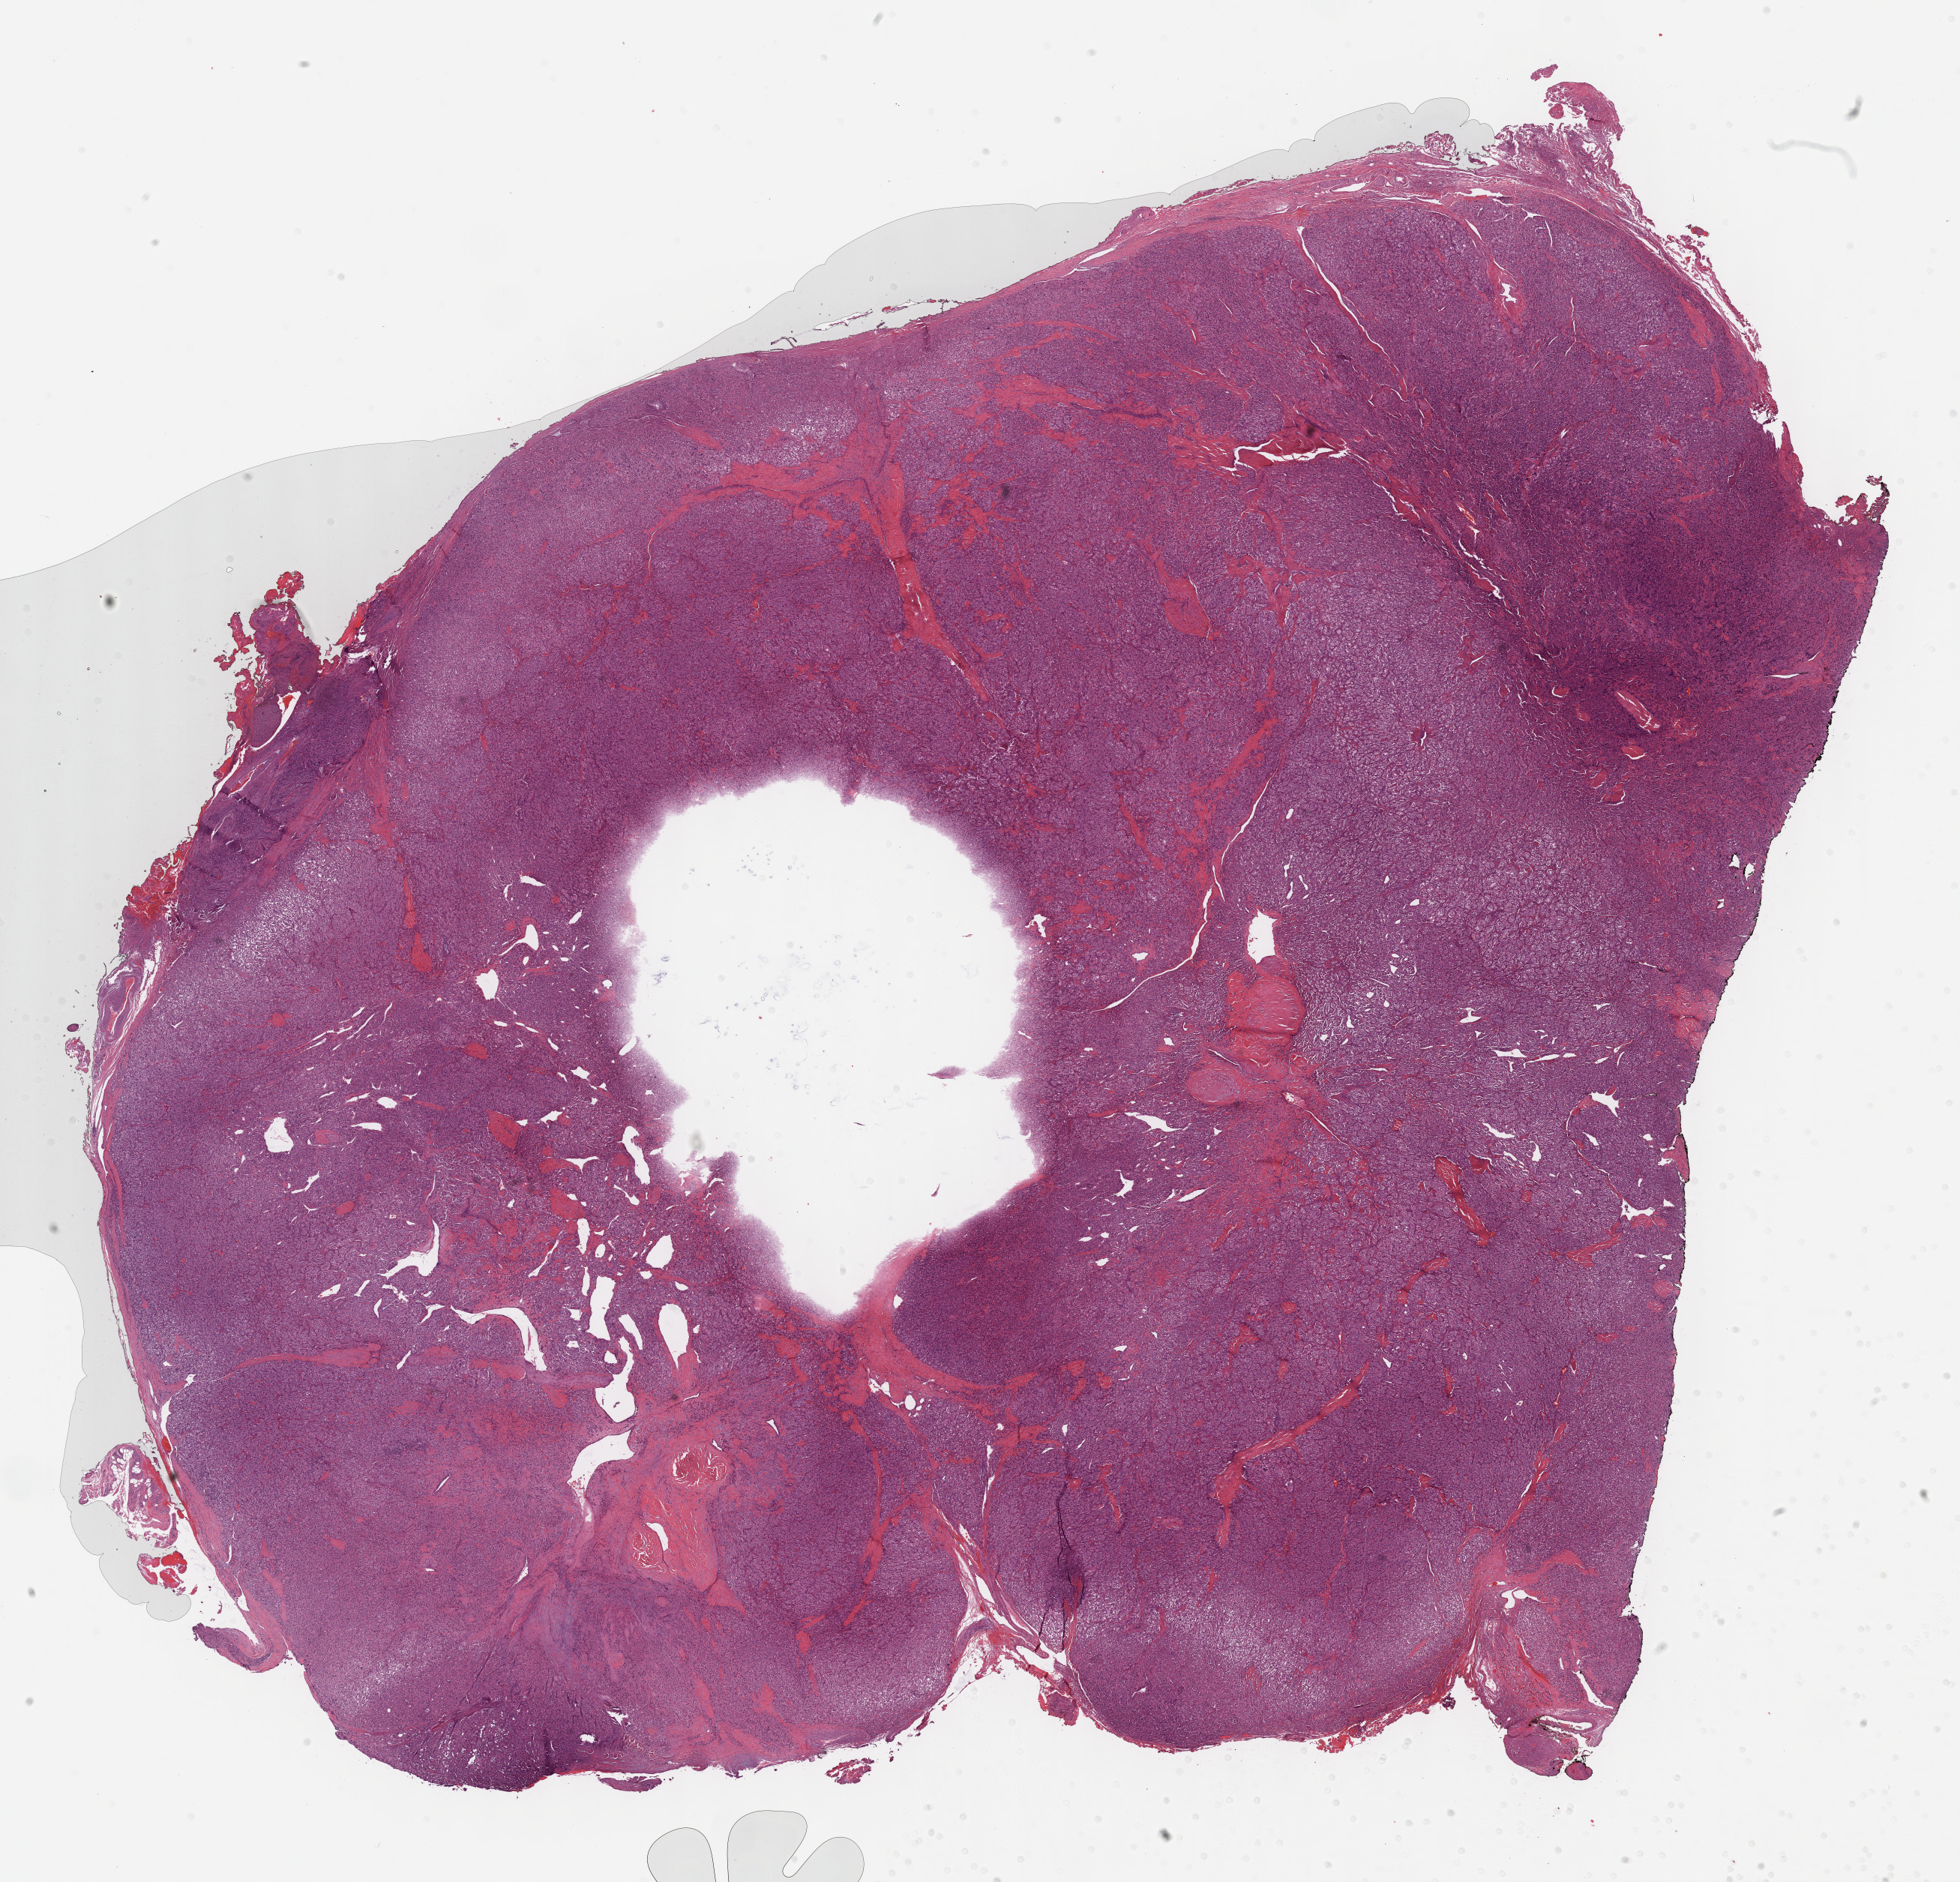
Digitized H&E-stained tissue section (whole slide), whole scanned area (about 21.1 x 20.3 mm, slide scanned at 40x) shown as a low-resolution overview. Formalin-fixed paraffin-embedded (FFPE) diagnostic section. Primary tumour sample. Male, age 46 years at initial diagnosis.
• pathologic diagnosis: Extra-adrenal paraganglioma, malignant (head, face or neck, NOS)